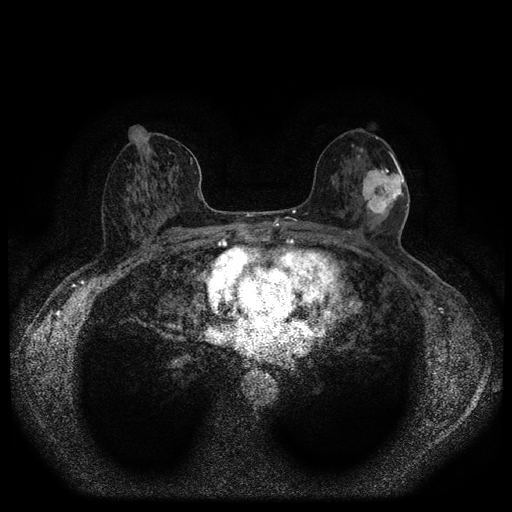
Breast MRI (dynamic contrast-enhanced, multi-phase), one axial slice. Position 55 of 116 along the scan axis. Dynamic contrast-enhanced series, time point 2 of 5 at this slice position (early post-contrast). 1.5 T. TE 2.7 ms, TR 5.4 ms. 512 × 512 image matrix, field of view 330 × 330 mm. Female patient, age 56 years.
Outlined on this slice (semi-automatically segmented with operator editing):
- breast lesion (labelled 'tumour' in the annotation; benign lesions carry a separate 'benign' label): bounding box <362,163,404,217> (left, top, right, bottom; pixels)